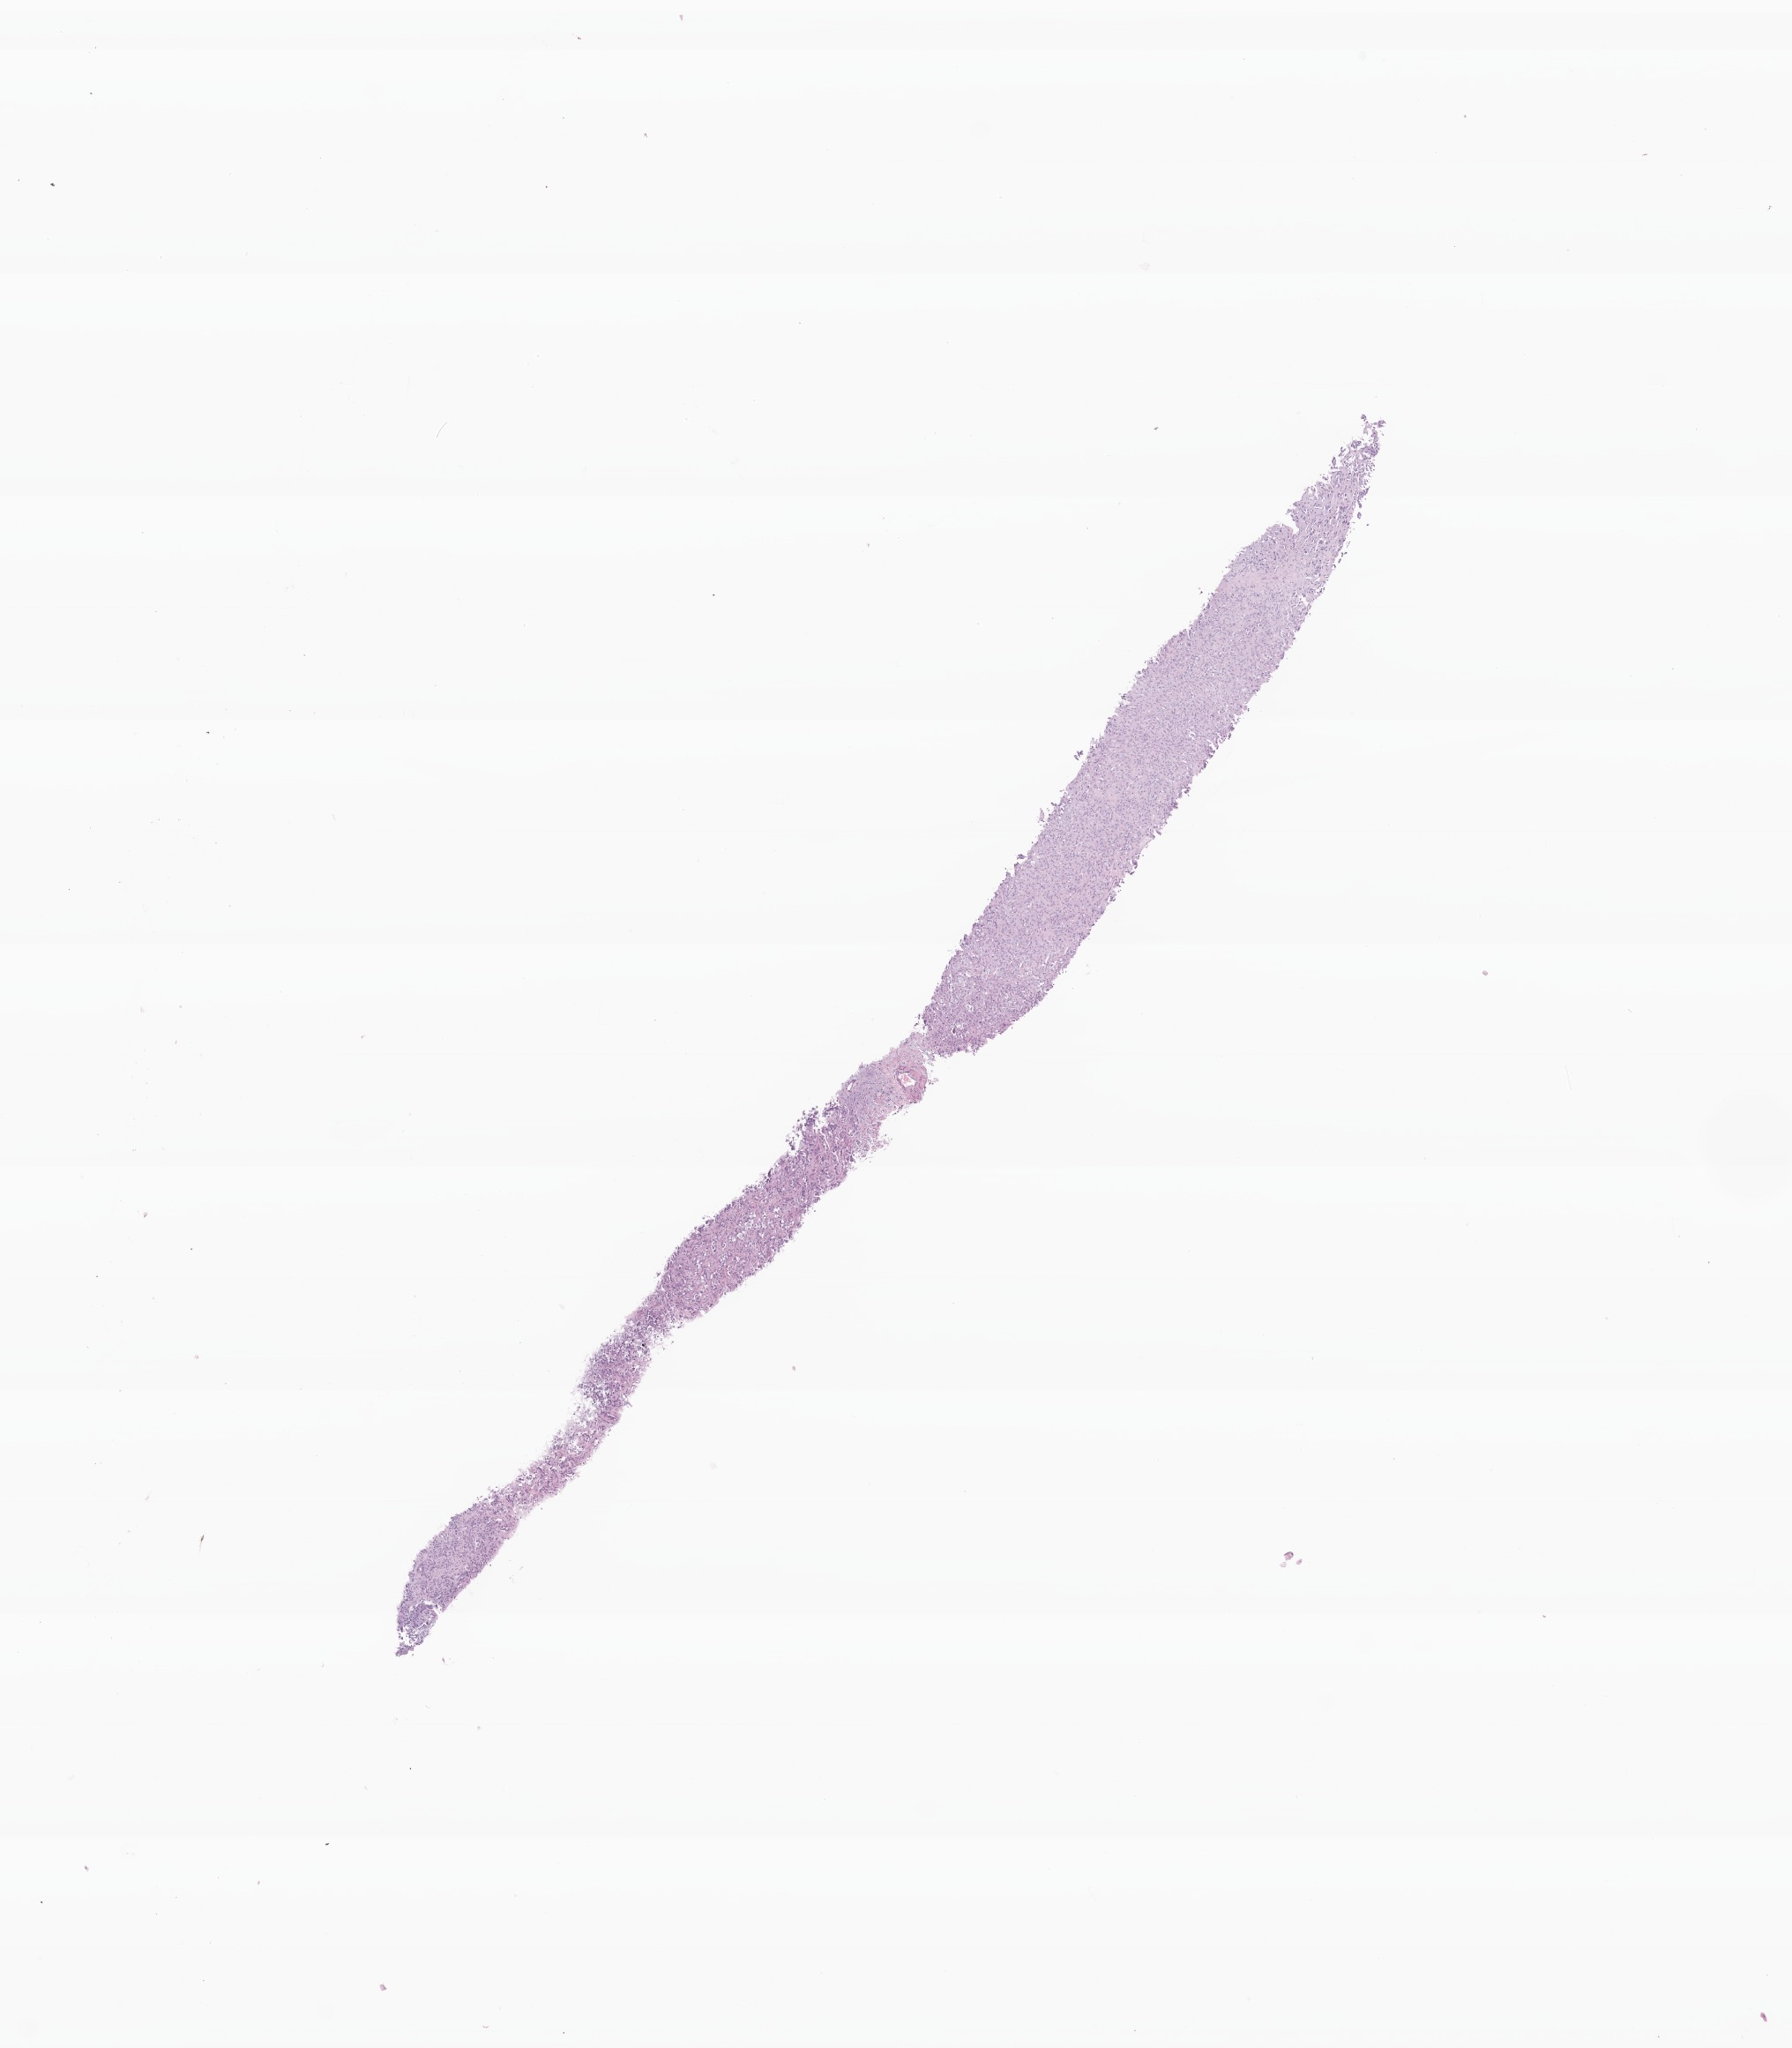
Digitized H&E-stained section of tumor tissue from the lung — whole scanned area (about 8.5 x 9.8 mm) shown as a low-resolution overview; formalin-fixed, paraffin-embedded (FFPE) tissue. Patient: male, age 180 months.
Diagnosis (ICD-O-3 morphology term): Adenocarcinoma, NOS.